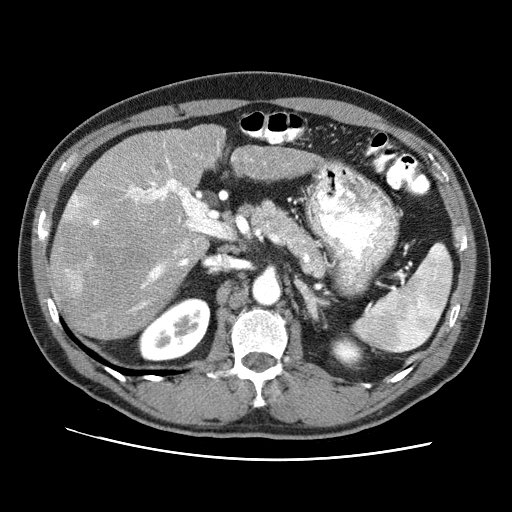
Contrast-enhanced abdominal CT (liver protocol), one axial slice. Position 44 of 71 along the scan axis. 120 kVp. Soft-tissue window (W 400 / L 40 HU). 2.5 mm slice thickness. 512 × 512 image matrix. From the clinical record (not read from this slice): diagnosis: hepatocellular carcinoma (patient treated with transarterial chemoembolisation; whether this scan precedes or follows treatment is not stated here); TNM stage (as recorded): Stage-II; Child-Pugh class: A; tumour differentiation: well differentiated; tumour nodularity: multinodular.
Structures marked on this image (semi-automatic segmentation, software-assisted and operator-edited):
- liver parenchyma outside the tumour (the mass and vessels are separate outlines, so this box may not span the whole liver): bounding box [x1, y1, x2, y2] px = [50, 124, 327, 340]
- mass: [50, 194, 98, 302]
- liver vessels: [92, 159, 197, 309]